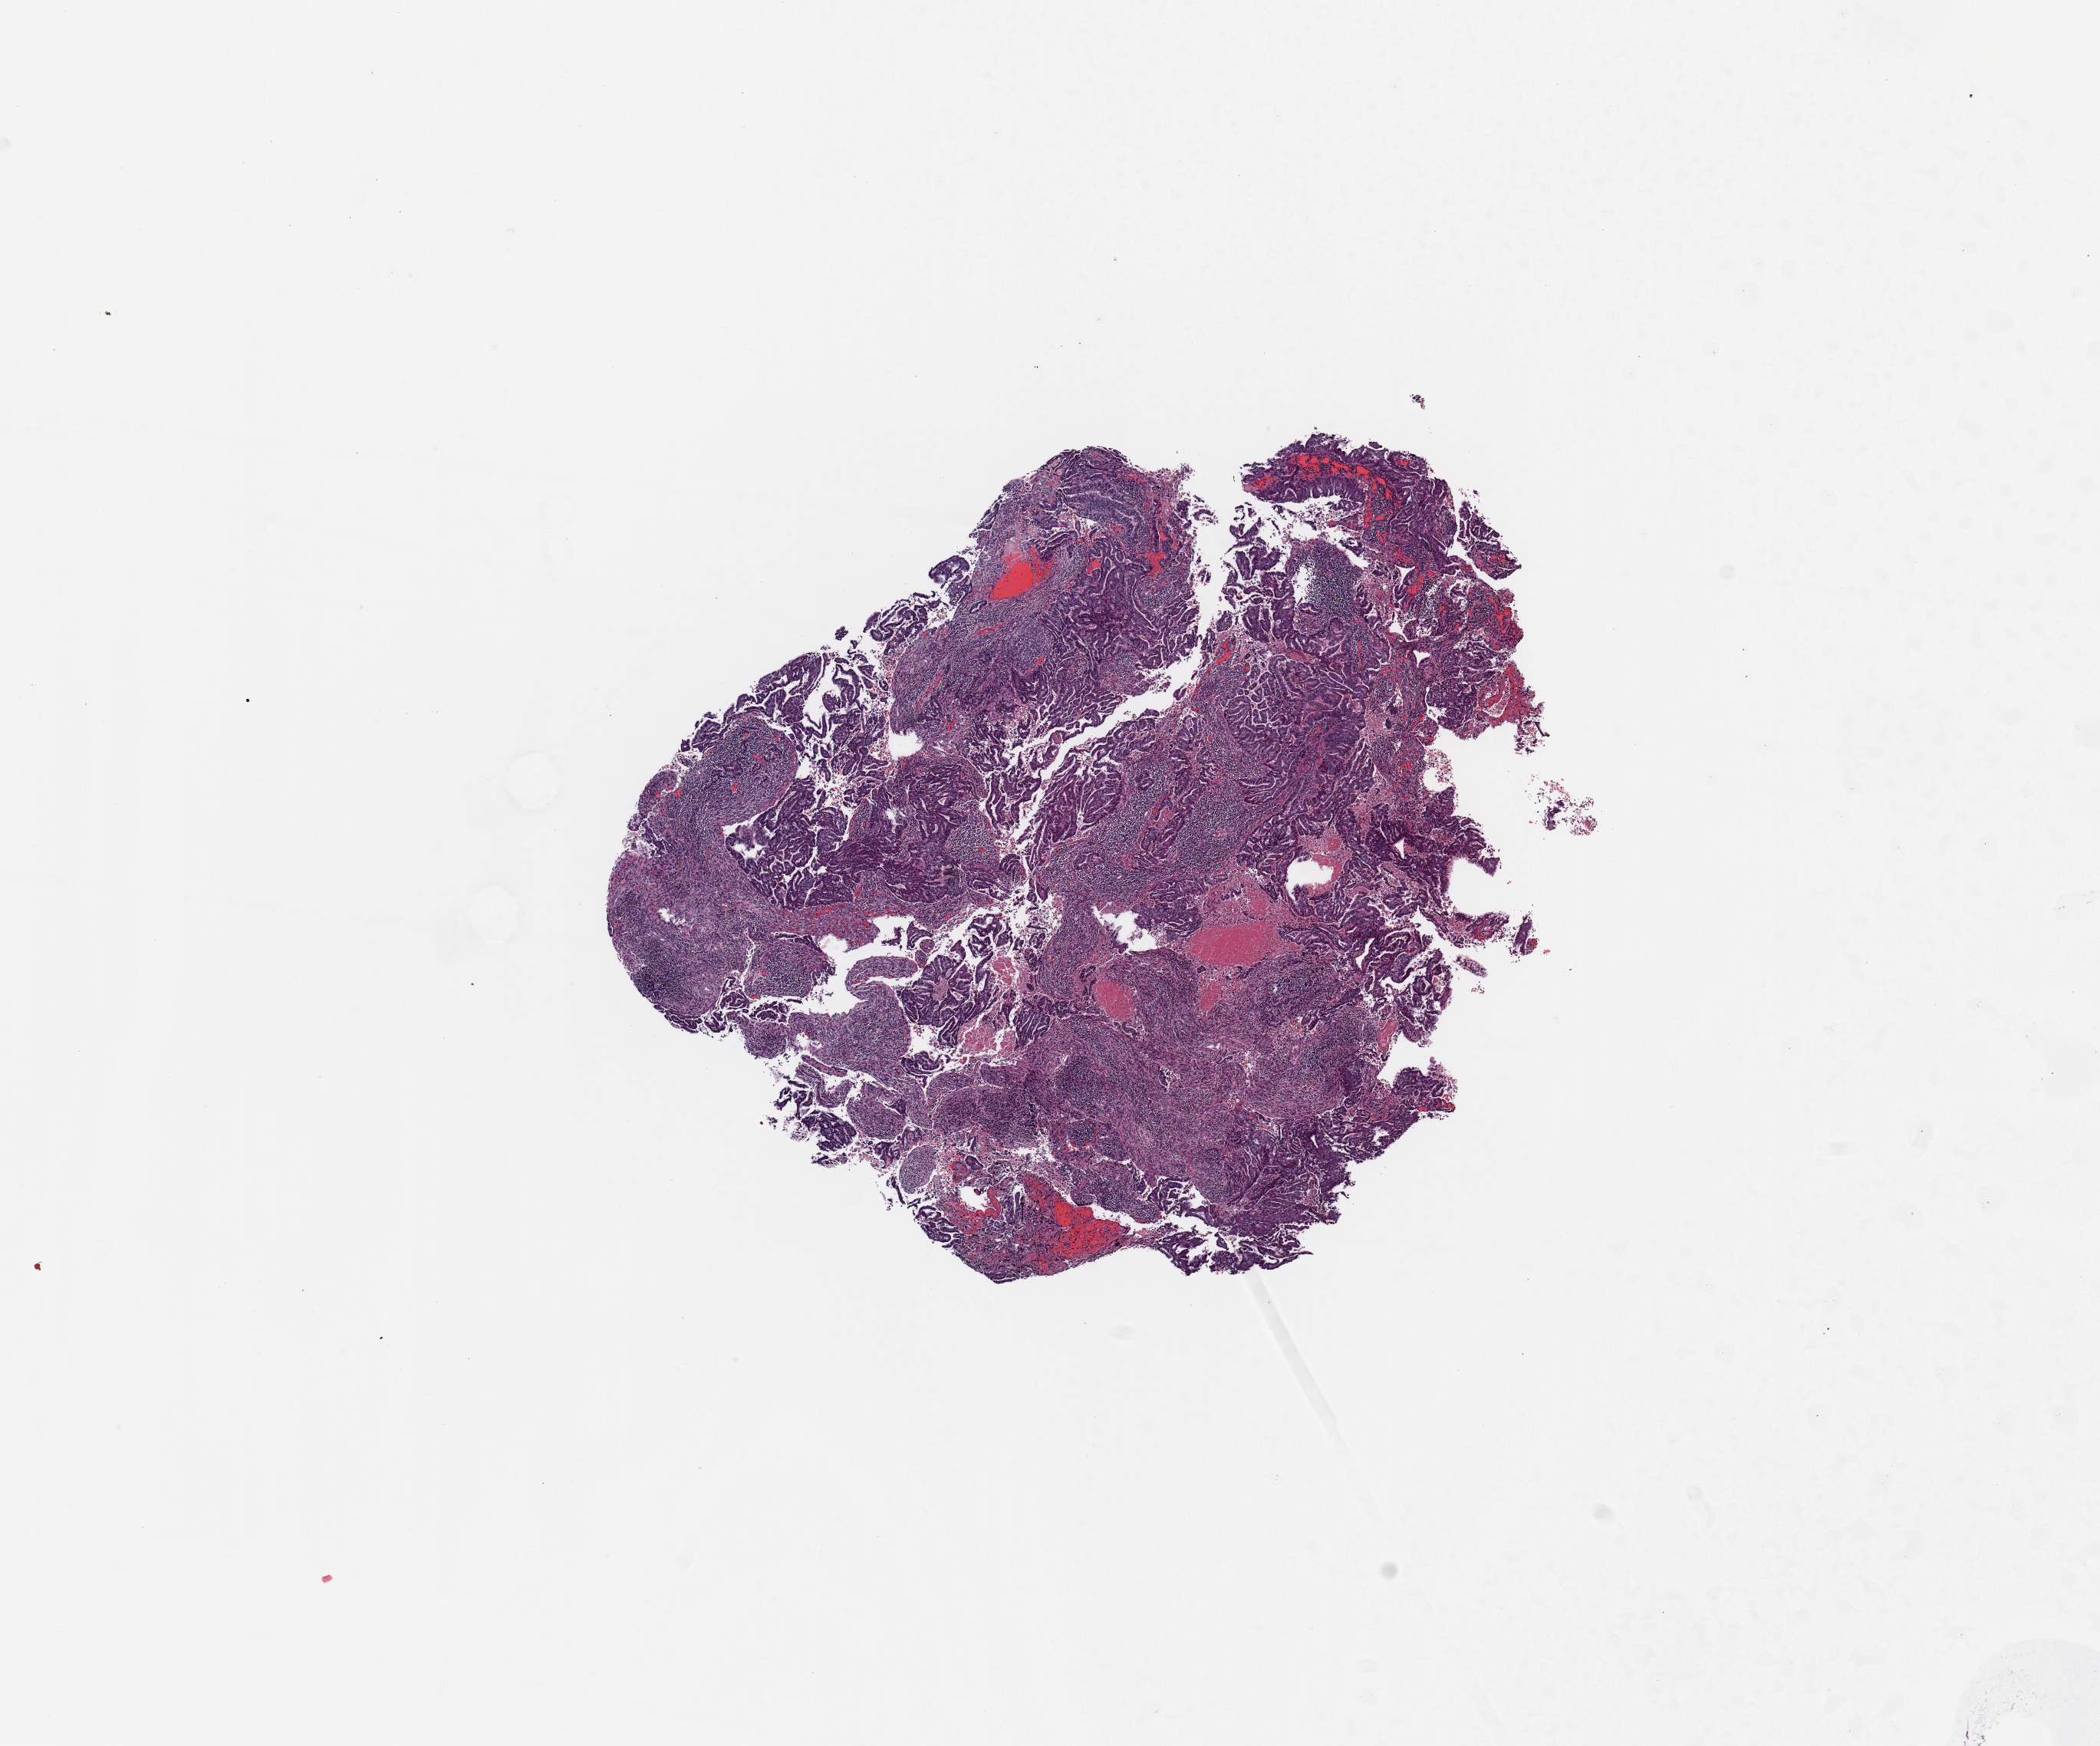
Digitized H&E tissue section (whole slide), shown as a low-resolution overview of the whole scanned area (about 10.8 x 9.0 mm, from a 20x scan). Tumour tissue sample, uterus. 48-year-old female patient. Histologic grade: G3 (poorly differentiated).
* diagnosis: Endometrioid adenocarcinoma, NOS
* AJCC pathologic stage: II